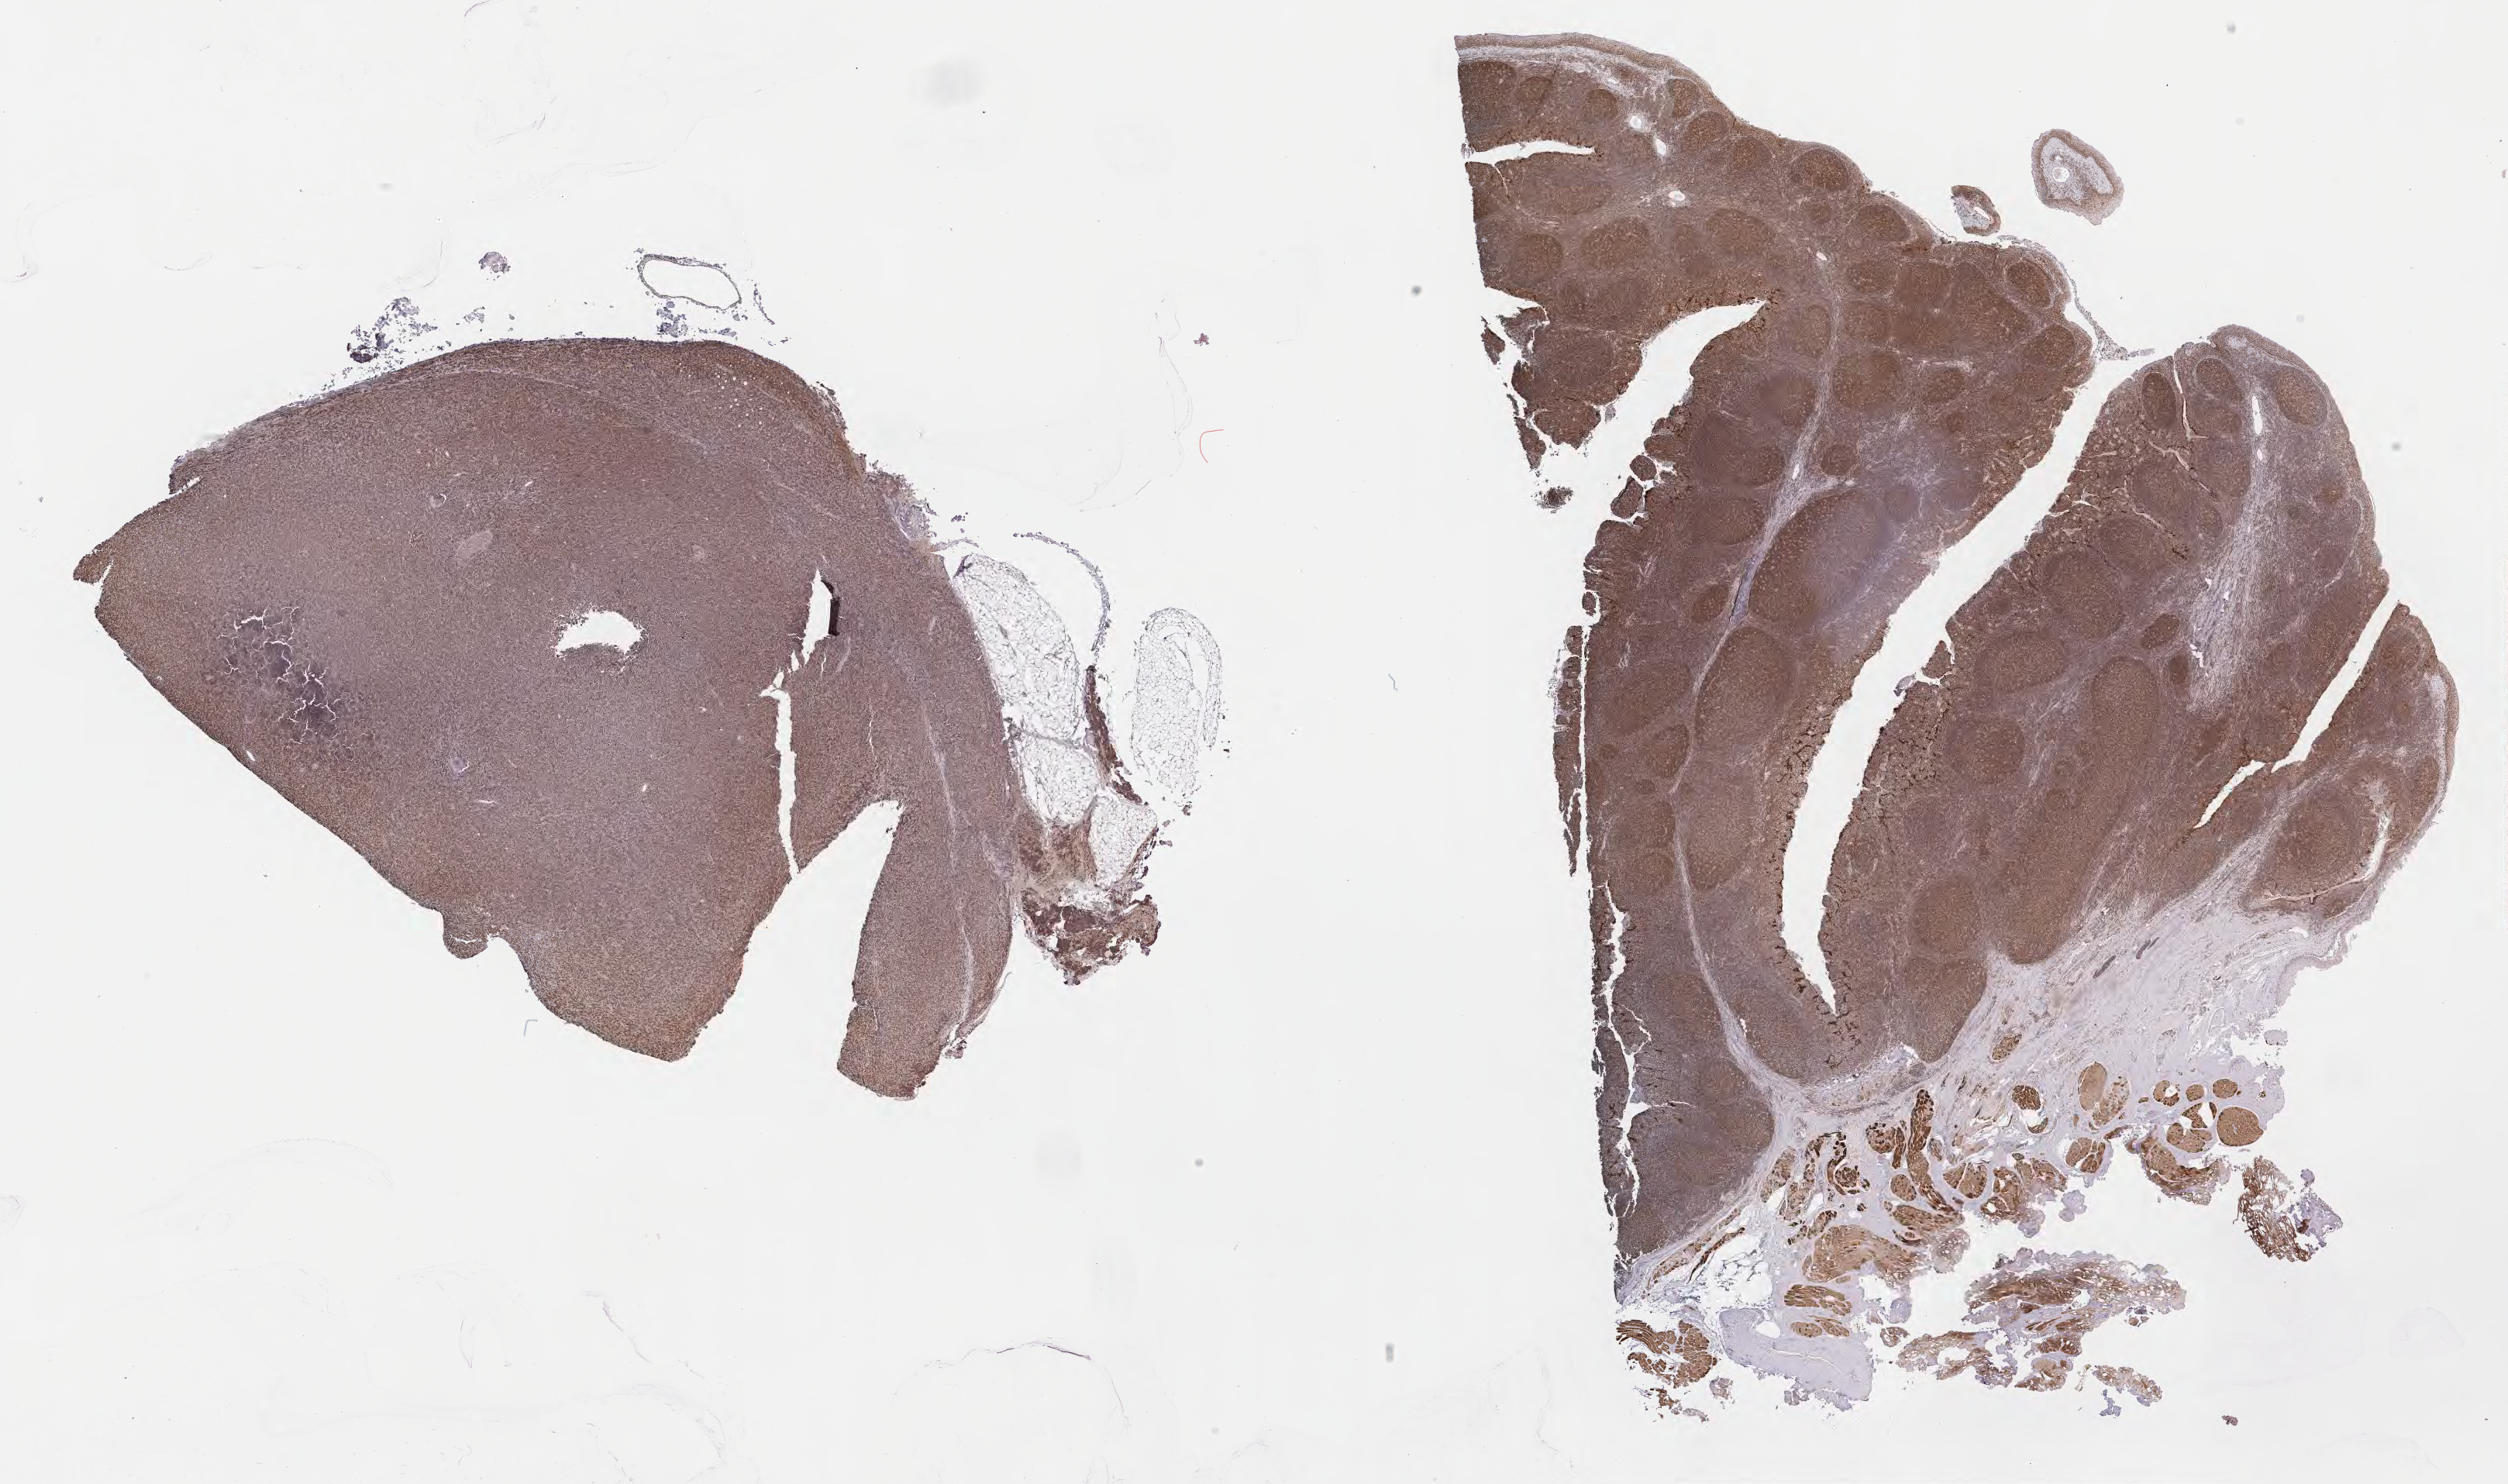
Whole-slide image, immunohistochemical stain for BCL6 — whole scanned area (about 26.2 x 15.5 mm) shown as a low-resolution overview, tumor tissue, site: lymph node. Patient male; 26 years old.
Diagnosis: Diffuse large B-cell lymphoma, NOS.